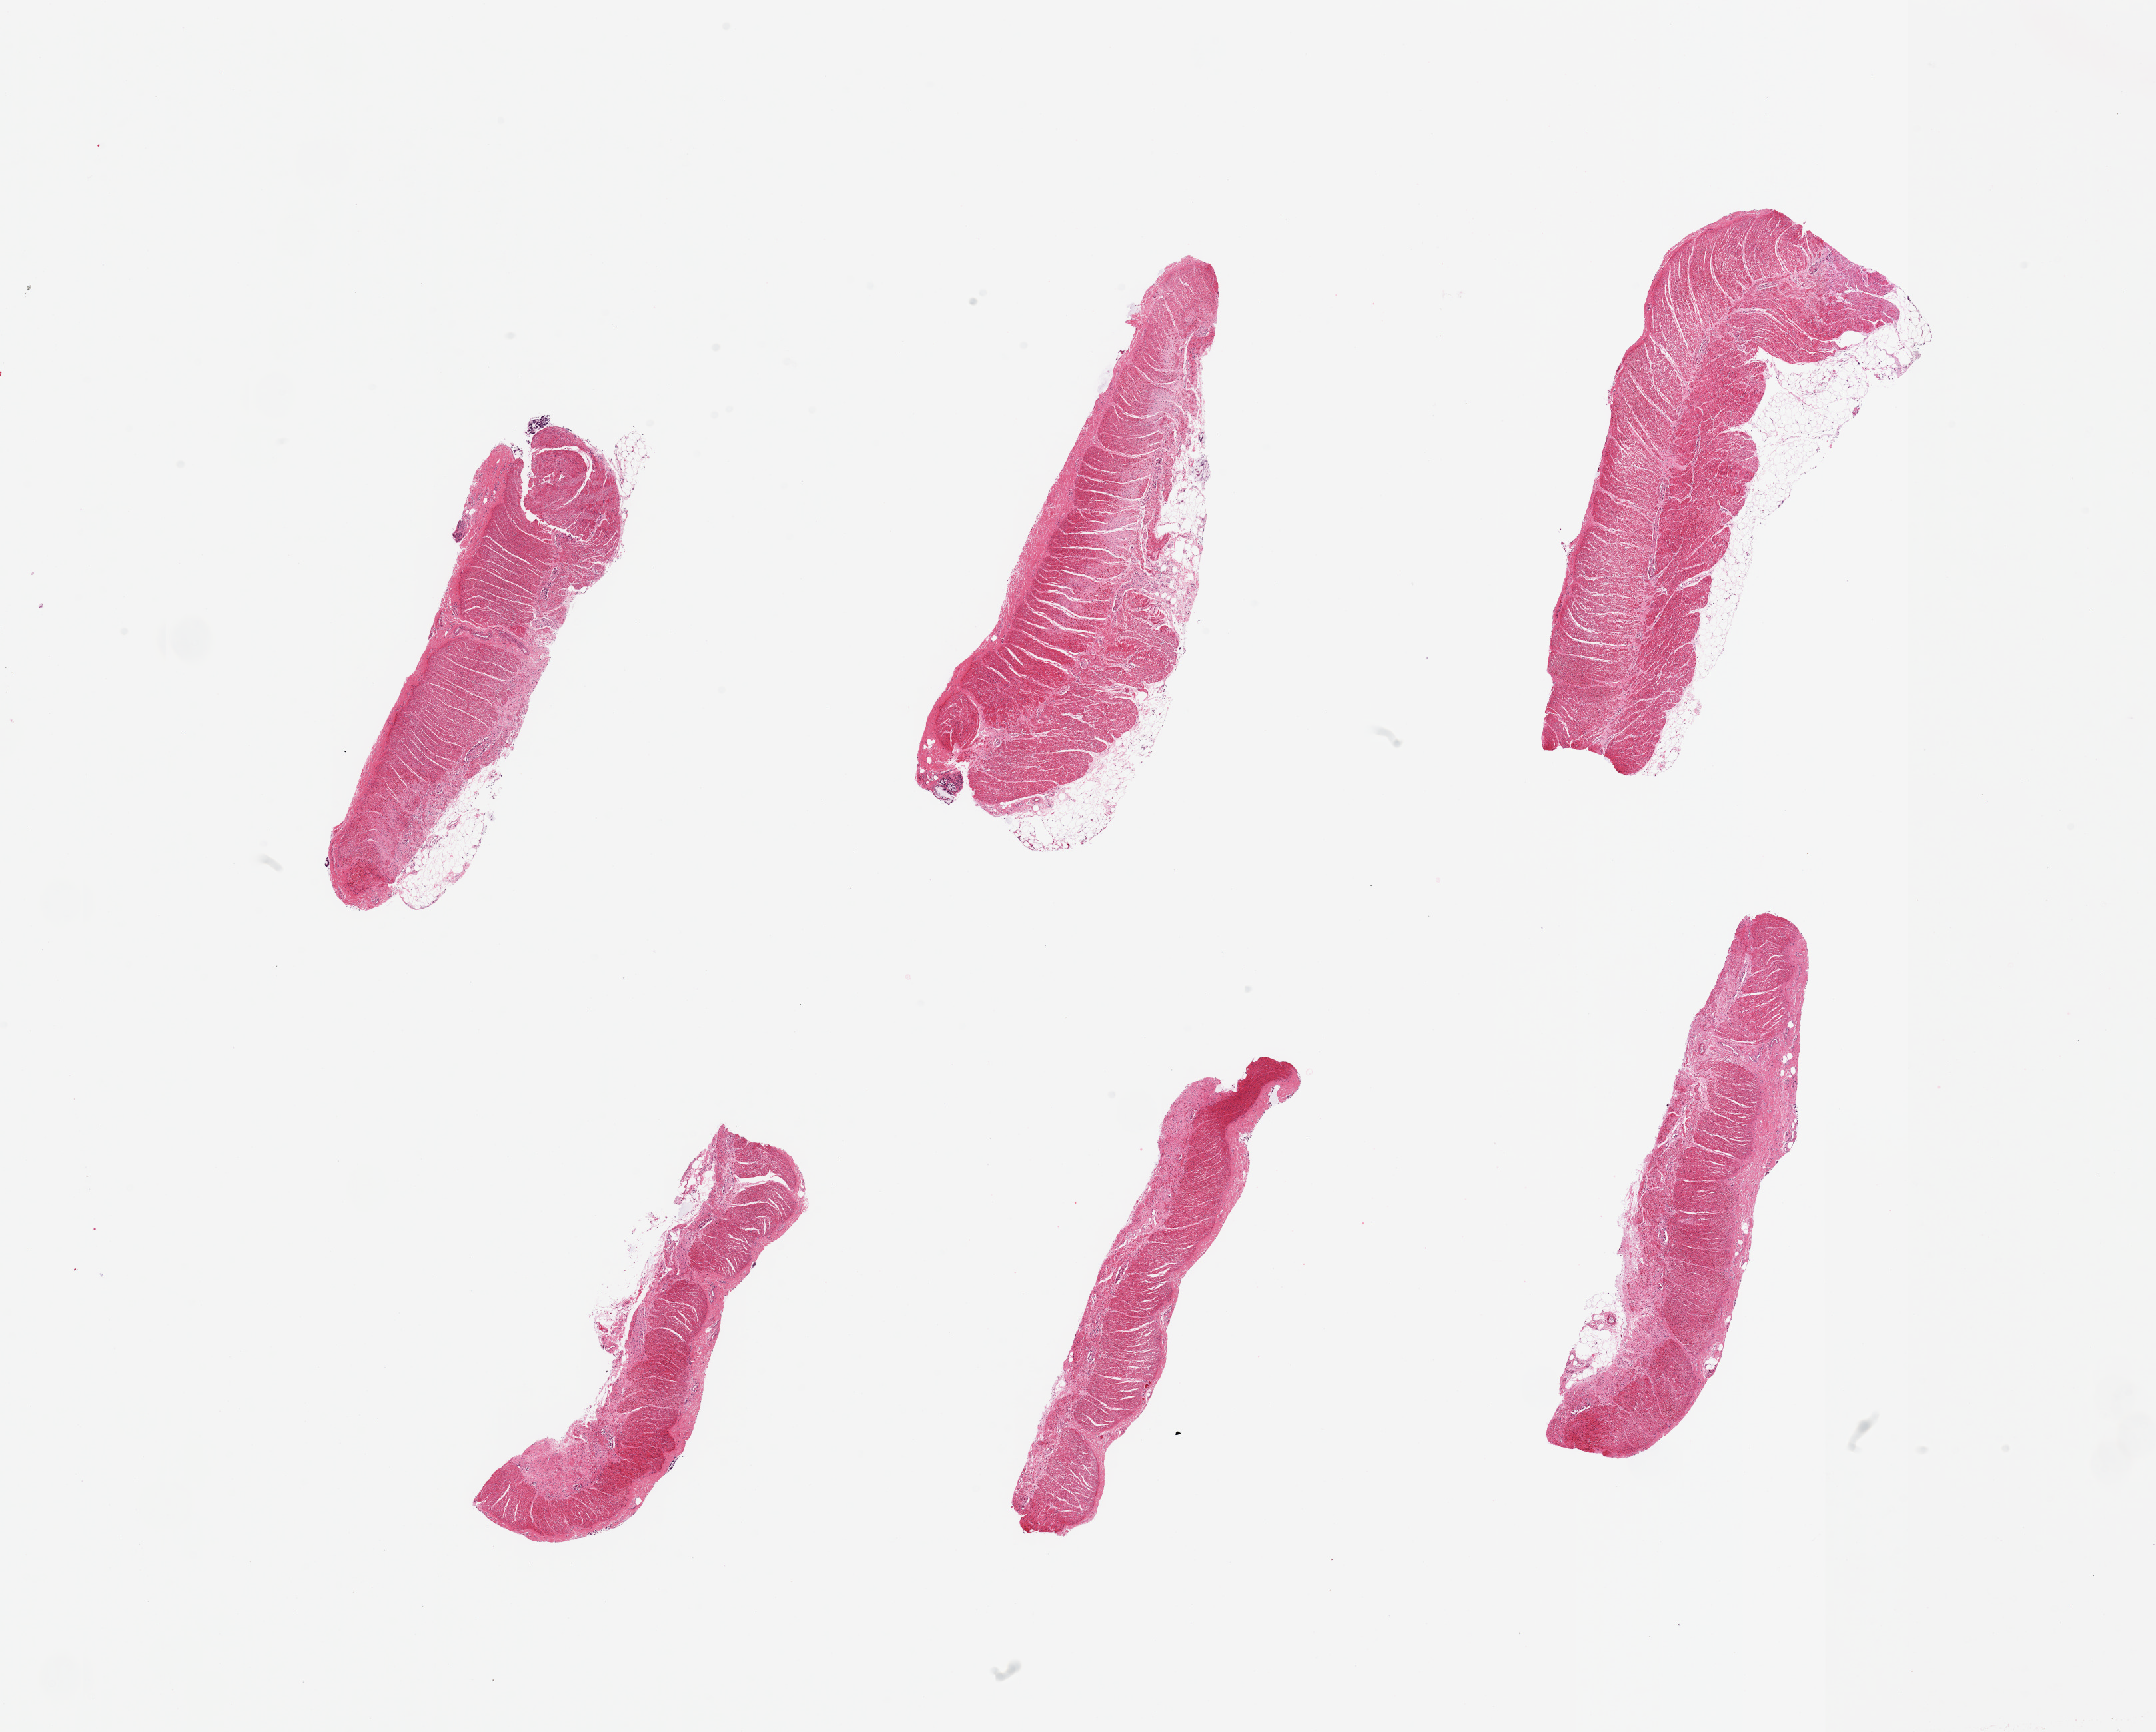
Hematoxylin and eosin (H&E) whole-slide image — low-resolution overview of the scanned area, about 25.6 x 20.6 mm, PAXgene-fixed, paraffin-embedded tissue, target tissue: sigmoid colon, donor tissue sample. Male donor.
* review note (as recorded): 6 pieces; well dissected muscularis